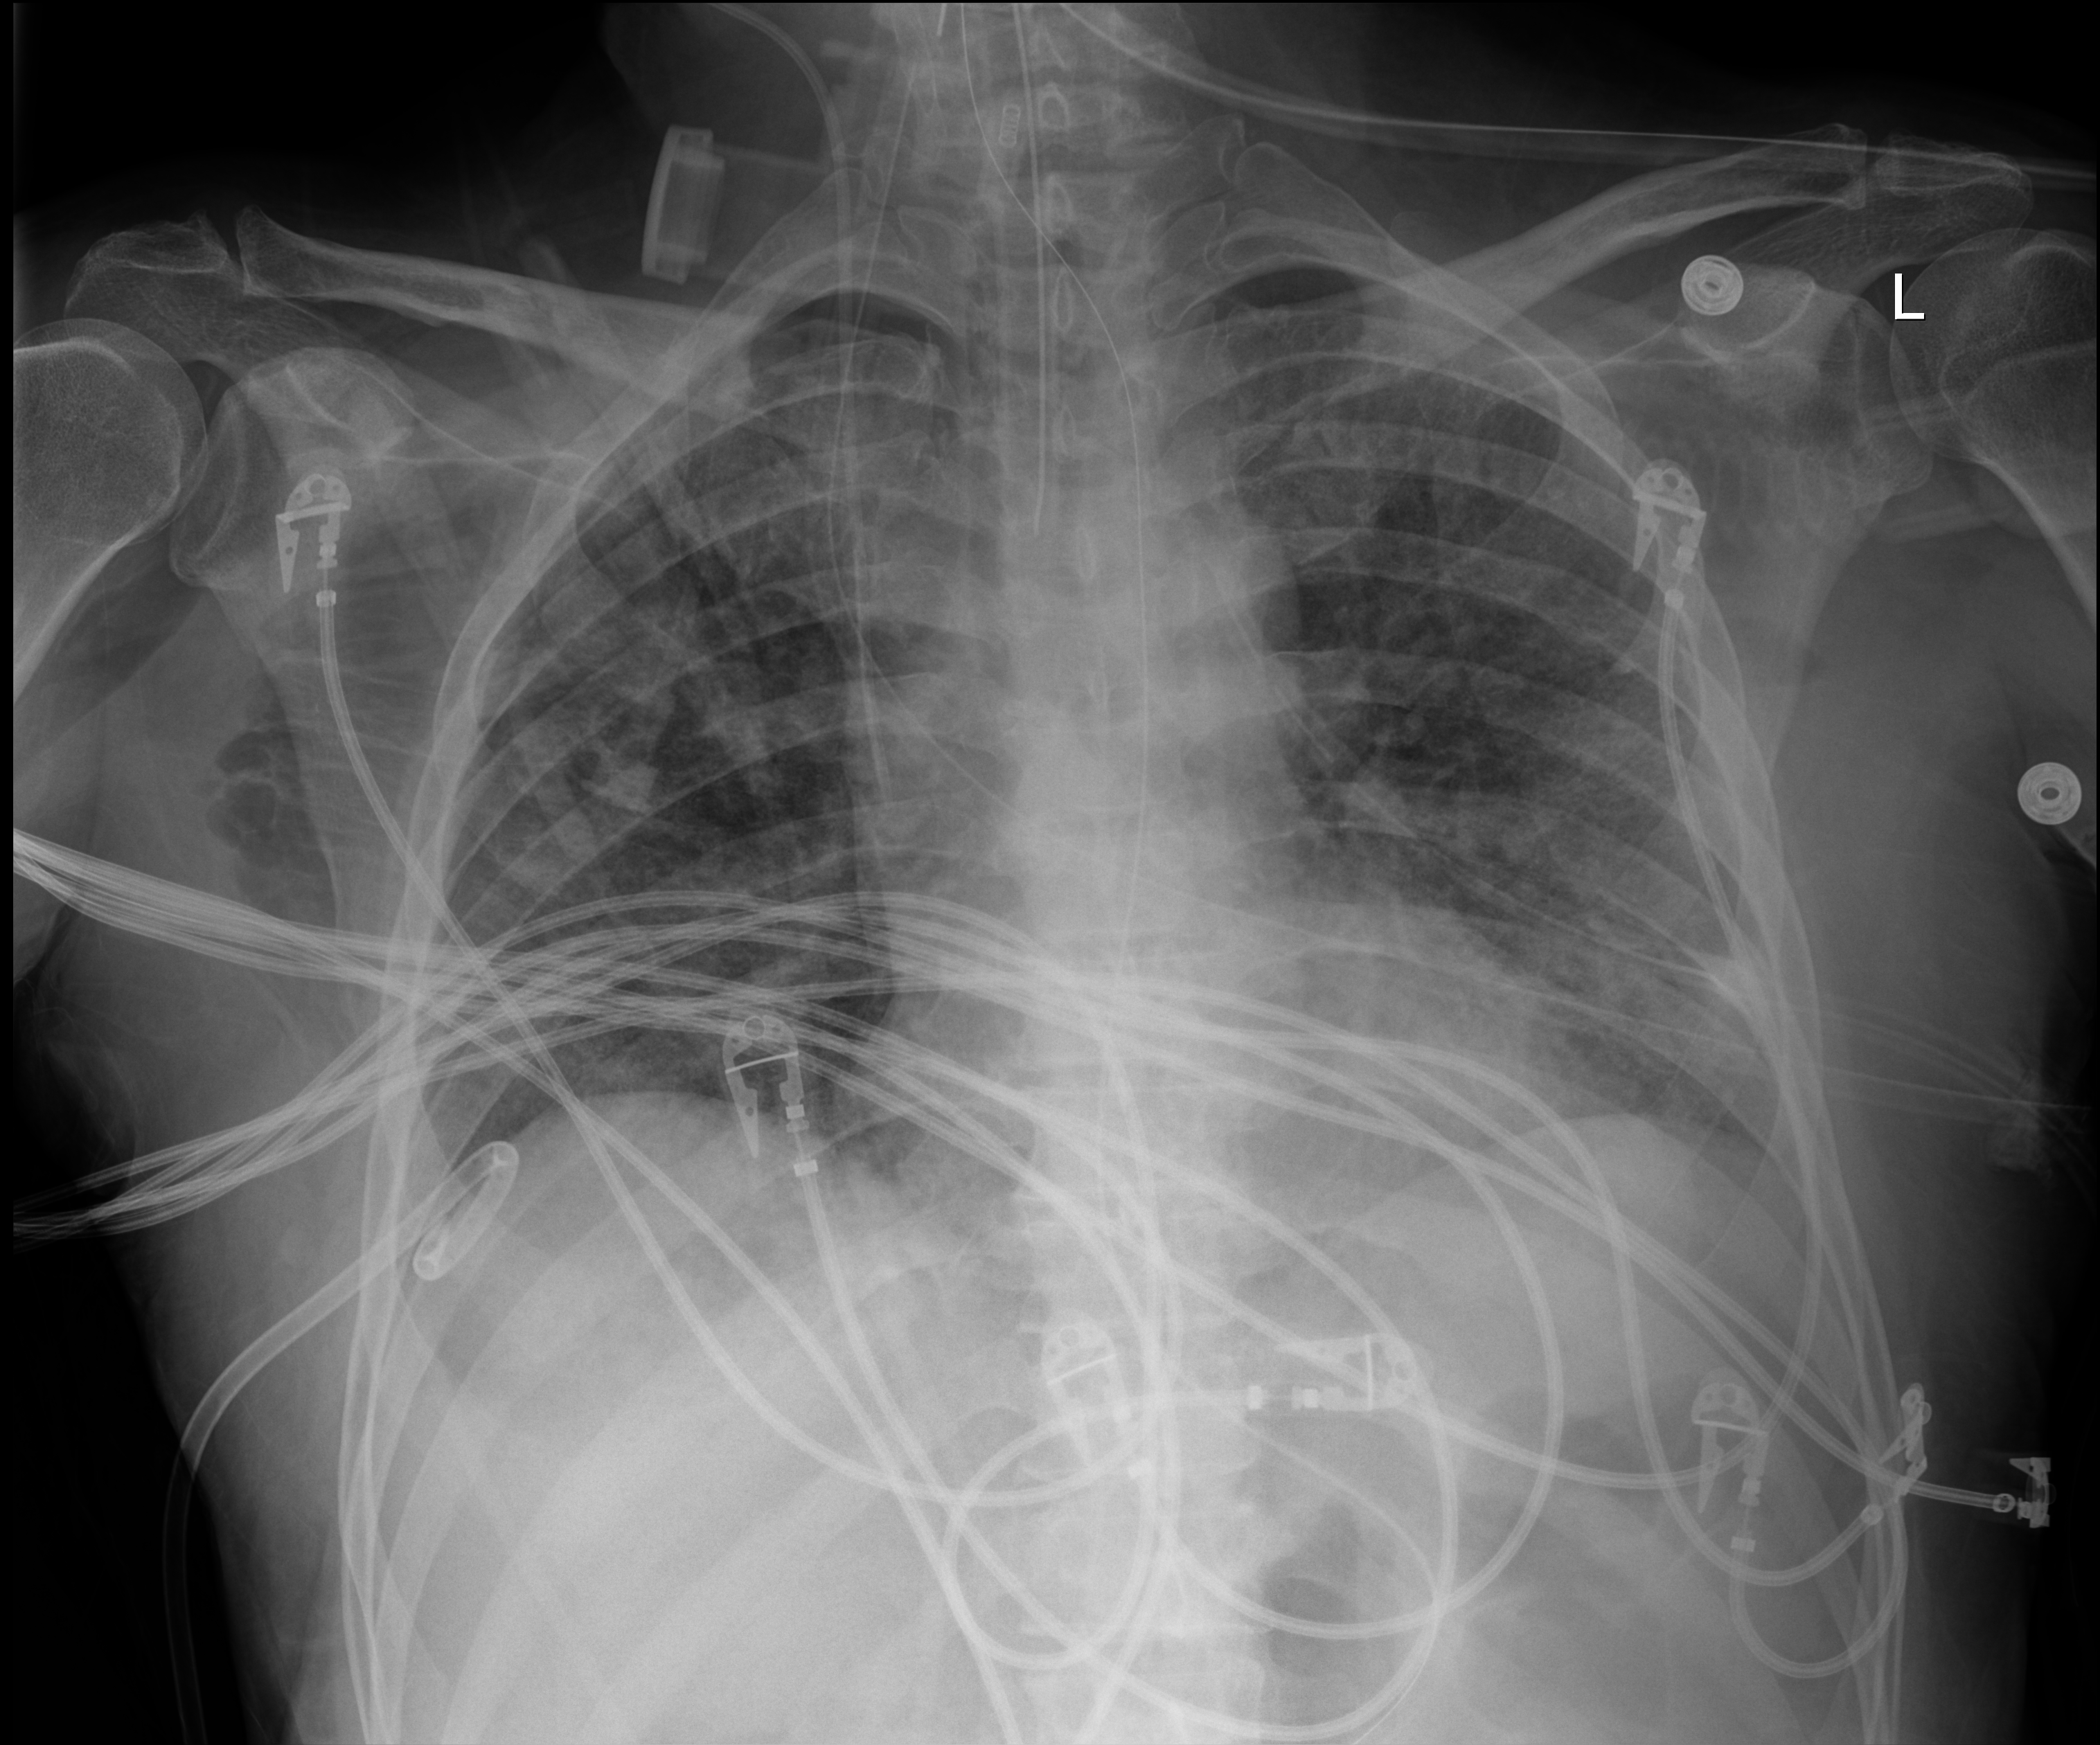
Bedside chest radiograph (digital radiography); anteroposterior (AP) projection. Patient hospitalised with COVID-19; male, aged 18–59 years.
From the hospital-stay record, not from the radiograph (when in the stay this image was taken is not recorded):
- hypertension (admission record): no
- admitted to intensive care during this hospital stay: yes
- mechanically ventilated during this hospital stay: yes